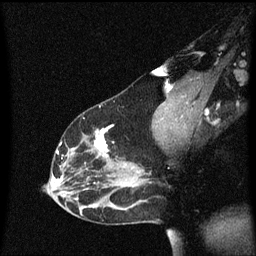
Breast MRI (dynamic contrast-enhanced), one sagittal slice. Position 37 of 60 along the scan axis. Dynamic contrast-enhanced series, image 2 of 3 at this slice position (ordered by acquisition). 1.5 T. TE 4.2 ms, TR 8.4 ms. 256 × 256 image matrix. Female patient, age 33 years.
Outlined on this slice (semi-automatically segmented with operator editing):
- analysis volume of interest (the breast-tissue region the enhancement analysis was run in; not a lesion): bounding box [x1, y1, x2, y2] px = [45, 116, 151, 191]
- tumour enhancement mask (voxels above the 70 % enhancement threshold inside the analysis volume of interest): [57, 126, 113, 185]